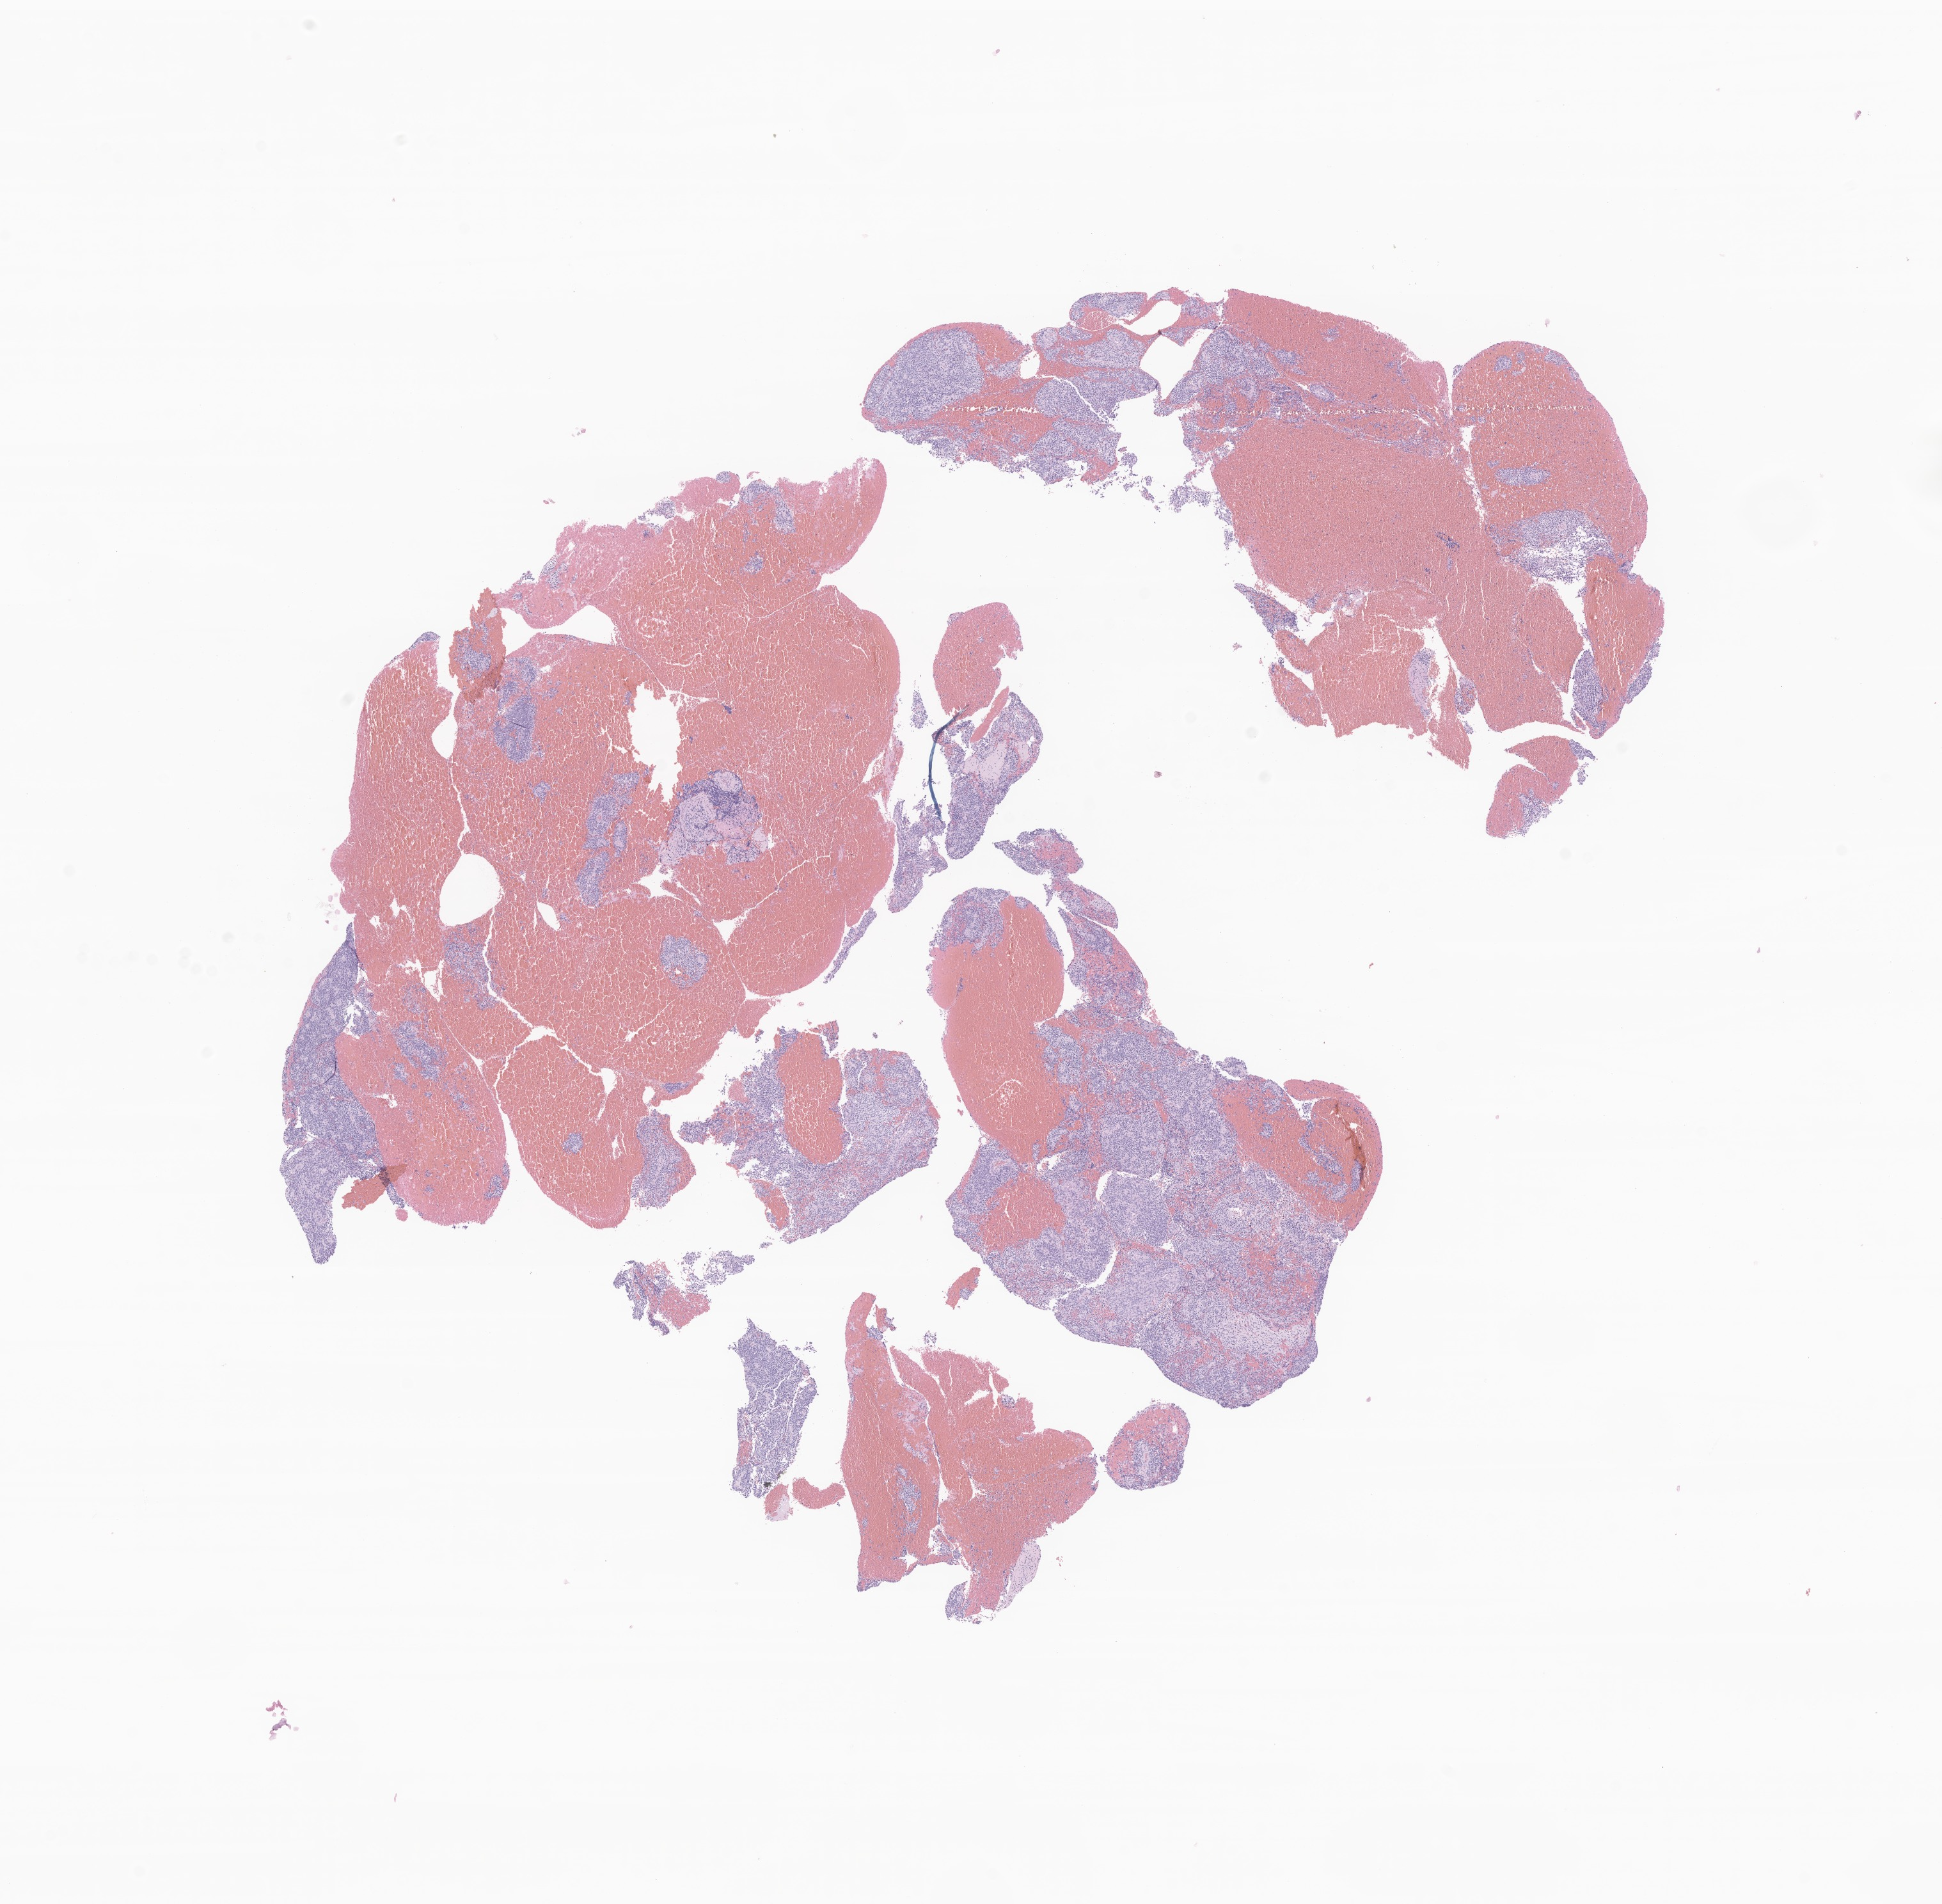
Digitized hematoxylin and eosin (H&E)-stained section of tumor tissue from the brain stem, a low-resolution overview of the entire scanned area, about 12.8 x 12.5 mm, FFPE section. Female patient, age 106 months (8 years 10 months).
- diagnosis: Glioma, malignant